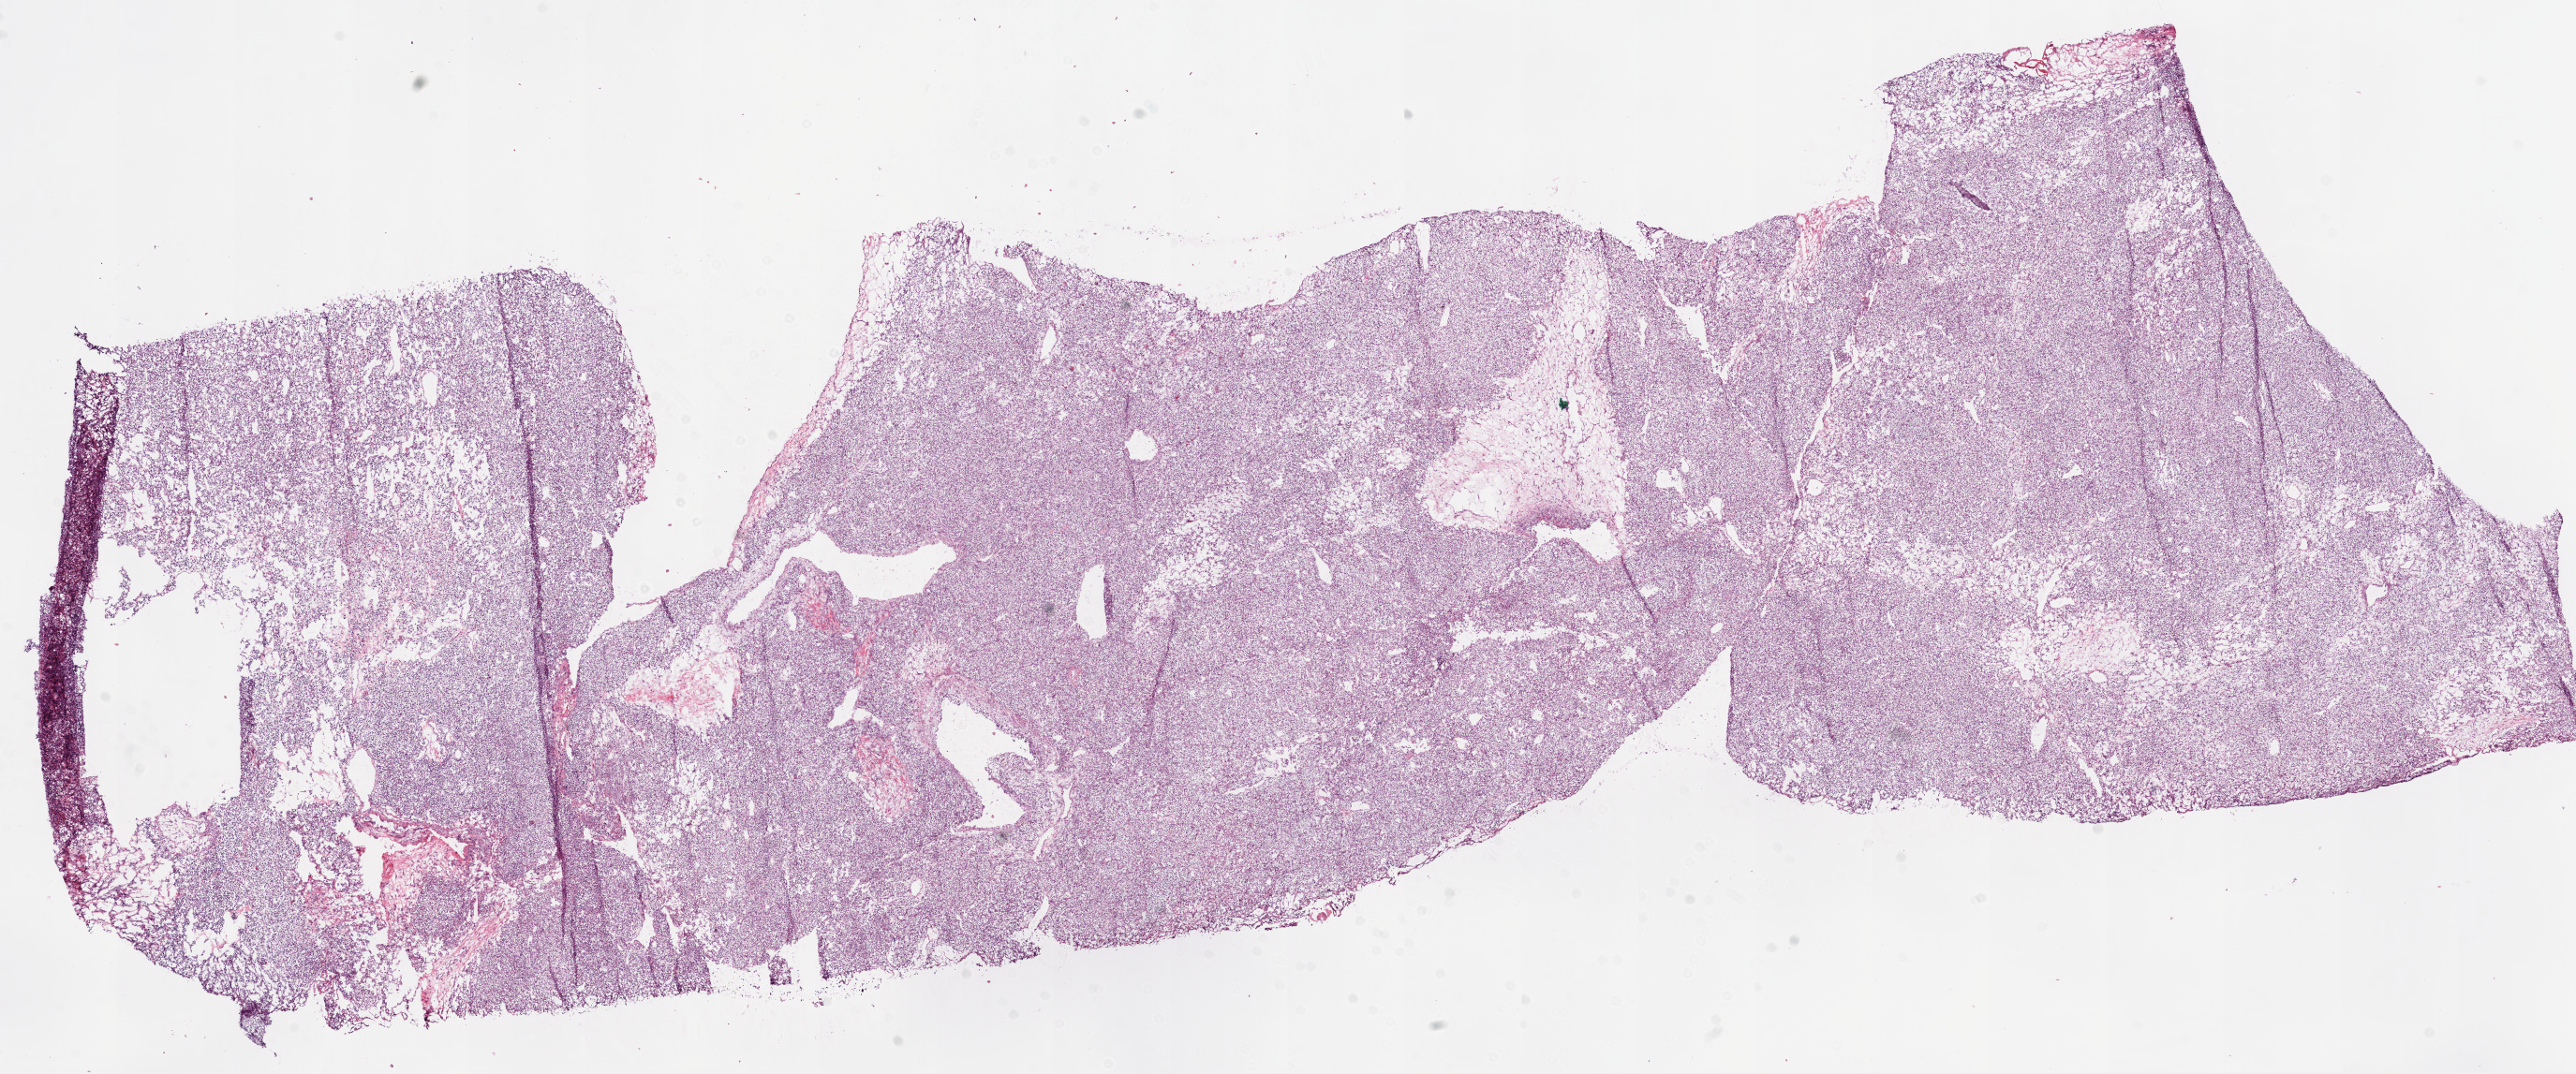
Digitized H&E tissue section (whole slide) — a low-resolution overview of the entire scanned area, about 22.1 x 9.2 mm (slide scanned at 20x), frozen section, sample: primary tumour, kidney. Female, age 62 years at initial diagnosis. Histologic grade: G2 (moderately differentiated). Slide review estimates, as recorded: tumour cells 90%, tumour nuclei 85%, normal cells 0%, stromal cells 10%, necrosis 0%.
- pathologic diagnosis: Clear cell adenocarcinoma, NOS
- AJCC pathologic stage: I